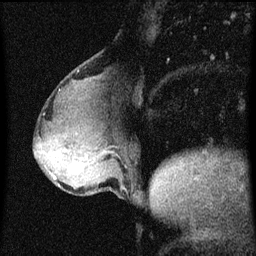
Breast MRI (dynamic contrast-enhanced), one sagittal slice. Position 24 of 60 along the scan axis. Dynamic contrast-enhanced series, image 2 of 3 at this slice position (ordered by acquisition). 1.5 T. TE 4.2 ms, TR 8 ms. 2 mm slice thickness. 256 × 256 image matrix, field of view 180 × 180 mm. Patient: female, 49 years.
Outlined on this slice (semi-automatically segmented with operator editing):
- analysis volume of interest (the breast-tissue region the enhancement analysis was run in; not a lesion): bounding box [x1, y1, x2, y2] px = [51, 158, 96, 185]
- tumour enhancement mask (voxels above the 70 % enhancement threshold inside the analysis volume of interest): [55, 166, 78, 179]